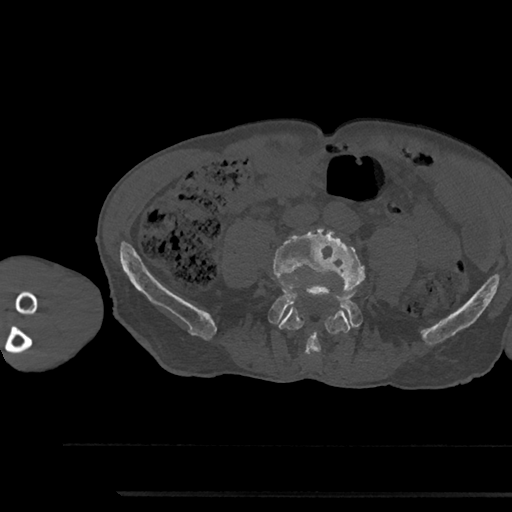
CT including the spine, one axial slice; position 384 of 797 along the scan axis; reconstruction kernel Br40s/3; 120 kVp; bone window (W 1800 / L 400 HU); 0.5 mm slice thickness; 512 × 512 image matrix, field of view 367 × 367 mm. Patient: male, 79 years. From the clinical record (not read from this slice): primary cancer: prostate.
Structures marked on this image (semi-automatic segmentation, software-assisted and operator-edited):
- L4 vertebra: bounding box [x1, y1, x2, y2] px = [272, 228, 364, 355]
- L5 vertebra: [269, 295, 361, 328]